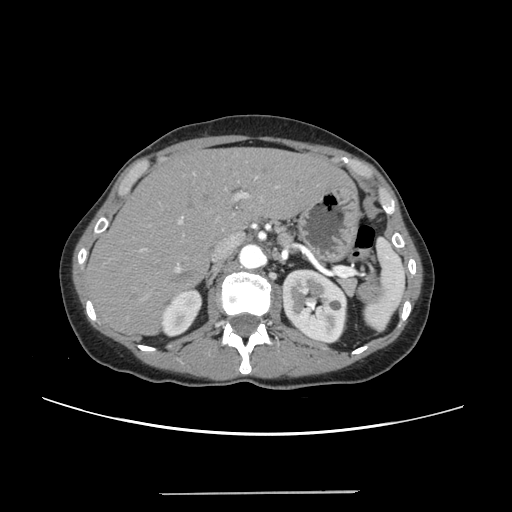
Contrast-enhanced abdominal CT, one axial slice. Position 161 of 240 along the scan axis. 120 kVp. Intravenous contrast given. Soft-tissue window (W 400 / L 40 HU). 1.25 mm slice thickness. 512 × 512 image matrix, field of view 371 × 371 mm. Female patient, age 60 years. Case-level facts recorded for this patient, not image findings: diagnosis: colorectal cancer liver metastases, imaged before liver resection; multiple liver metastases: no.
Annotated regions visible in this slice (manually delineated by an expert):
- liver: bounding box [x1, y1, x2, y2] px = [88, 148, 348, 334]
- planned liver remnant (the part of the liver to remain after resection): [88, 148, 347, 334]
- portal vein (with intrahepatic branches): [139, 171, 259, 272]